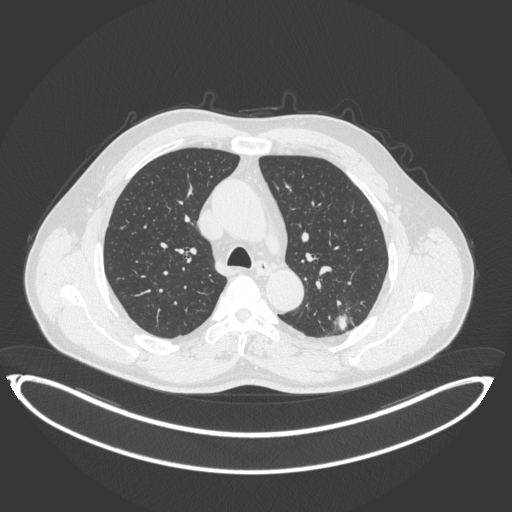
Chest CT, one axial slice. Position 246 of 399 along the scan axis. 120 kVp. Lung window (W 1500 / L -600 HU). 1 mm slice thickness. 512 × 512 image matrix, field of view 469 × 469 mm. Male patient, age 58 years. Case-level facts recorded for this patient, not image findings: clinical TNM (as recorded): T1c N0 M0; histopathological grade: G1-2.
Structures marked on this image (rectangle marked by the reading radiologist):
- lung tumour (recorded histology: adenocarcinoma): box from (x=325, y=311) to (x=358, y=337) px